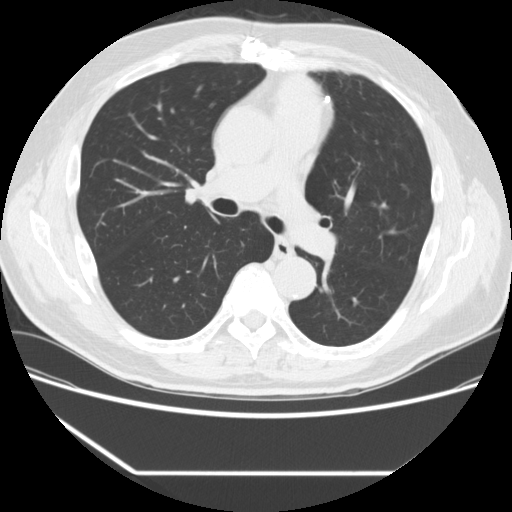
Chest CT (low-dose screening protocol), one axial image. First (baseline) screen. Lung window (W 1500 / L -600 HU). 2.5 mm slice thickness. Standard (soft-tissue) reconstruction kernel (STANDARD). 120 kVp. Slice 96 of 247 in the series. Male participant, aged 66 years at enrolment. Former smoker at enrolment.
Expert-annotated lung lesion, bounding box <322,172,350,196> (left, top, right, bottom; pixels). Reader record for this screening exam (exam-level; its link to the box is not recorded): non-calcified nodule or mass ≥4 mm, right lower lobe, 4 × 4 mm, smooth margins, soft tissue attenuation. Note: the box lies in the patient's left hemithorax on this image, whereas the reader's record names the right lung; they may be different findings. Participant outcome: lung cancer diagnosed 792 days after this screen — squamous cell carcinoma, NOS, left upper lobe, poorly differentiated (G3), stage IA (AJCC 6th edition), 27 mm at pathology.